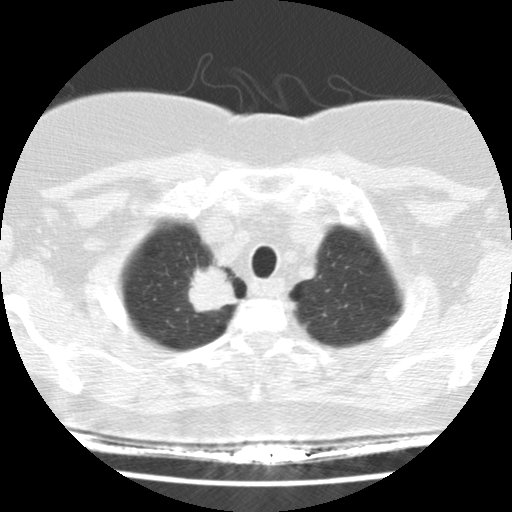
Low-dose screening chest CT, one axial slice. Slice 132 of 148 in the series (ordered by position). Reconstruction kernel STANDARD. 120 kVp. Lung window (W 1500 / L -600 HU). 2.5 mm slice thickness. 512 × 512 image matrix.
Outlined on this slice (expert manual segmentation):
- lesion 1 (tumor, upper lobe of right lung): bounding box (x1, y1, x2, y2) in pixels: (188, 263, 237, 312)